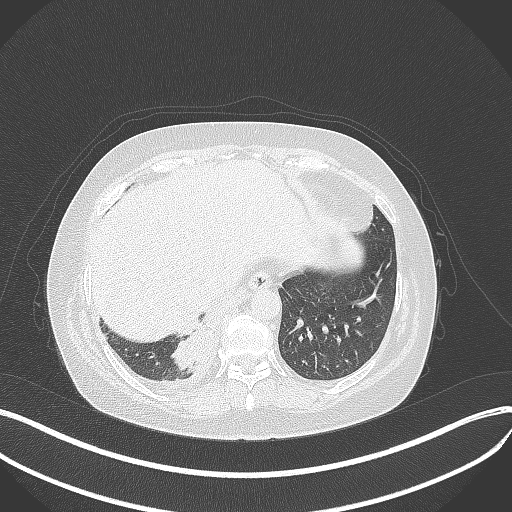
Chest CT, one axial slice. Position 86 of 381 along the scan axis. Lung window (W 1500 / L -600 HU). 1 mm slice thickness. 512 × 512 image matrix, field of view 400 × 400 mm. Female patient, age 56 years. Case-level facts recorded for this patient, not image findings: clinical TNM (as recorded): T2b N1 M0.
Outlined on this slice (bounding box drawn by a radiologist):
- lung tumour (recorded histology: small cell carcinoma): bounding box [x1, y1, x2, y2] px = [169, 329, 217, 370]